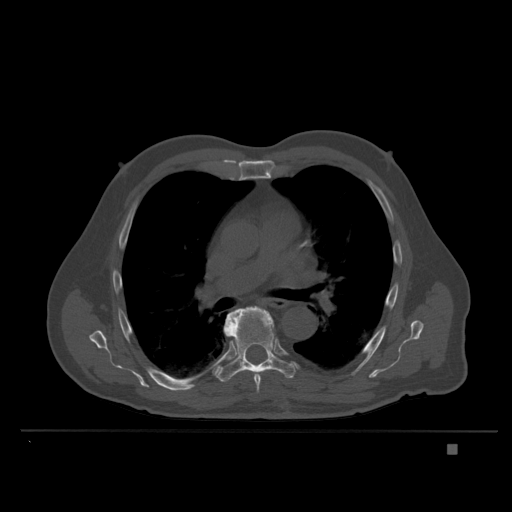
CT including the spine, one axial slice; position 248 of 435 along the scan axis; bone window (W 1800 / L 400 HU); 512 × 512 image matrix, field of view 434 × 434 mm. Patient: male, 73 years. From the clinical record (not read from this slice): primary cancer: skin.
Annotated regions visible in this slice (semi-automatically segmented with operator editing):
- T6 vertebra: bounding box <224,306,264,392> (left, top, right, bottom; pixels)
- T7 vertebra: <216,306,298,382>